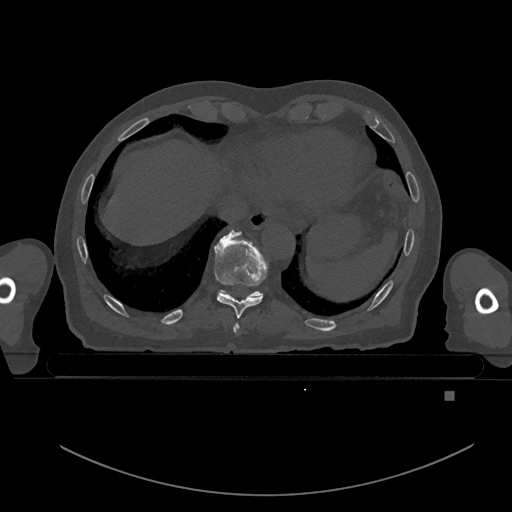
CT including the spine, one axial slice; slice 134 of 969 in the series (ordered by position); bone window (W 1800 / L 400 HU); 0.5 mm slice thickness; 512 × 512 image matrix. Patient: male, 82 years. From the clinical record (not read from this slice): primary cancer: prostate.
Structures marked on this image (semi-automatically segmented with operator editing):
- T10 vertebra: box from (x=253, y=291) to (x=261, y=296) px
- T8 vertebra: (x=233, y=323)–(x=239, y=333)
- T9 vertebra: (x=214, y=230)–(x=269, y=318)